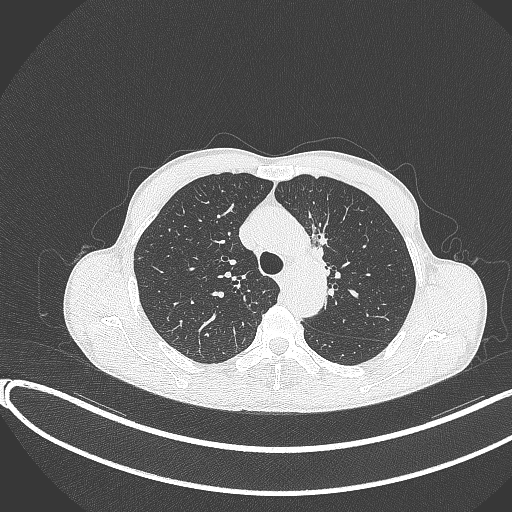
Chest CT, one axial slice; slice 272 of 374 in the series (ordered by position); reconstruction kernel B70f; 120 kVp; lung window (W 1500 / L -600 HU); 1 mm slice thickness; 512 × 512 image matrix. Patient: male, 58 years. From the clinical record (not read from this slice): clinical TNM (as recorded): T1c N1 M0.
Annotated regions visible in this slice (rectangle marked by the reading radiologist):
- lung tumour (recorded histology: adenocarcinoma): box from (x=301, y=217) to (x=334, y=271) px